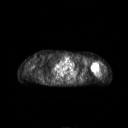
FDG PET of an extremity soft-tissue mass (from a PET/CT study), one axial slice; slice 180 of 267 in the series (ordered by position); 128 × 128 image matrix, field of view 700 × 700 mm. Female patient, age 83 years. Case-level facts recorded for this patient, not image findings: histological type: pleiomorphic leiomyosarcoma; grade: high; site of the primary tumour: left biceps.
Outlined on this slice (expert contour drawn on MRI and transferred to this co-registered scan by the dataset authors):
- gross tumour volume including surrounding oedema: bounding box <91,62,100,76> (left, top, right, bottom; pixels)
- gross tumour volume (mass): <91,62,100,73>